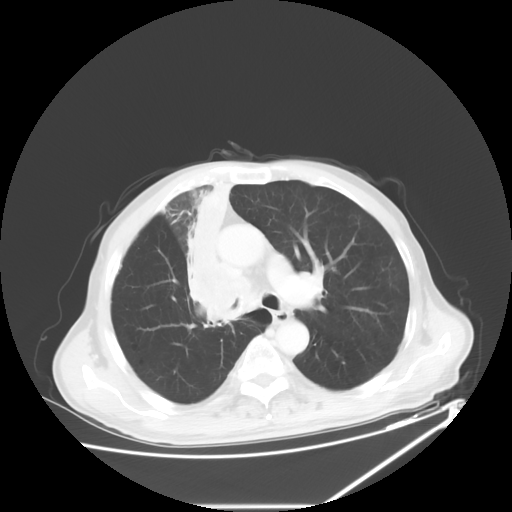
Chest CT, one axial slice. Position 40 of 60 along the scan axis. Reconstruction kernel STANDARD. 120 kVp. Lung window (W 1500 / L -600 HU). 5 mm slice thickness. 512 × 512 image matrix, field of view 410 × 410 mm. Patient: male, 73 years. From the clinical record (not read from this slice): clinical TNM (as recorded): T2a N1 M0.
Outlined on this slice (rectangle marked by the reading radiologist):
- lung tumour (recorded histology: squamous cell carcinoma): bounding box [x1, y1, x2, y2] px = [180, 177, 249, 333]